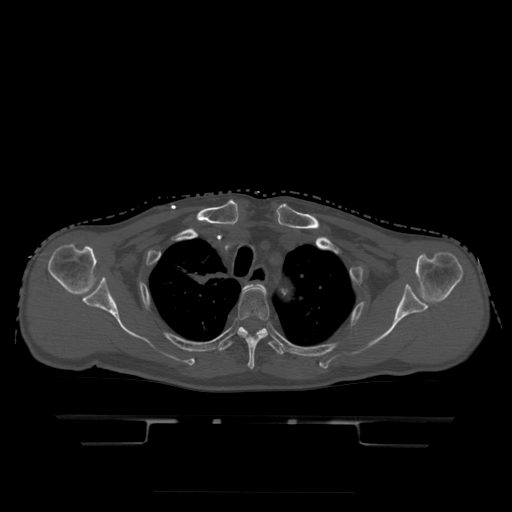
CT including the spine, one axial slice. Position 366 of 522 along the scan axis. Bone window (W 1800 / L 400 HU). 512 × 512 image matrix. Patient age 68 years. Case-level facts recorded for this patient, not image findings: primary cancer: urothelial.
Structures marked on this image (semi-automatically segmented with operator editing):
- T2 vertebra: bounding box (x1, y1, x2, y2) in pixels: (245, 286, 251, 289)
- T3 vertebra: (237, 285, 270, 370)
- T4 vertebra: (218, 327, 286, 356)